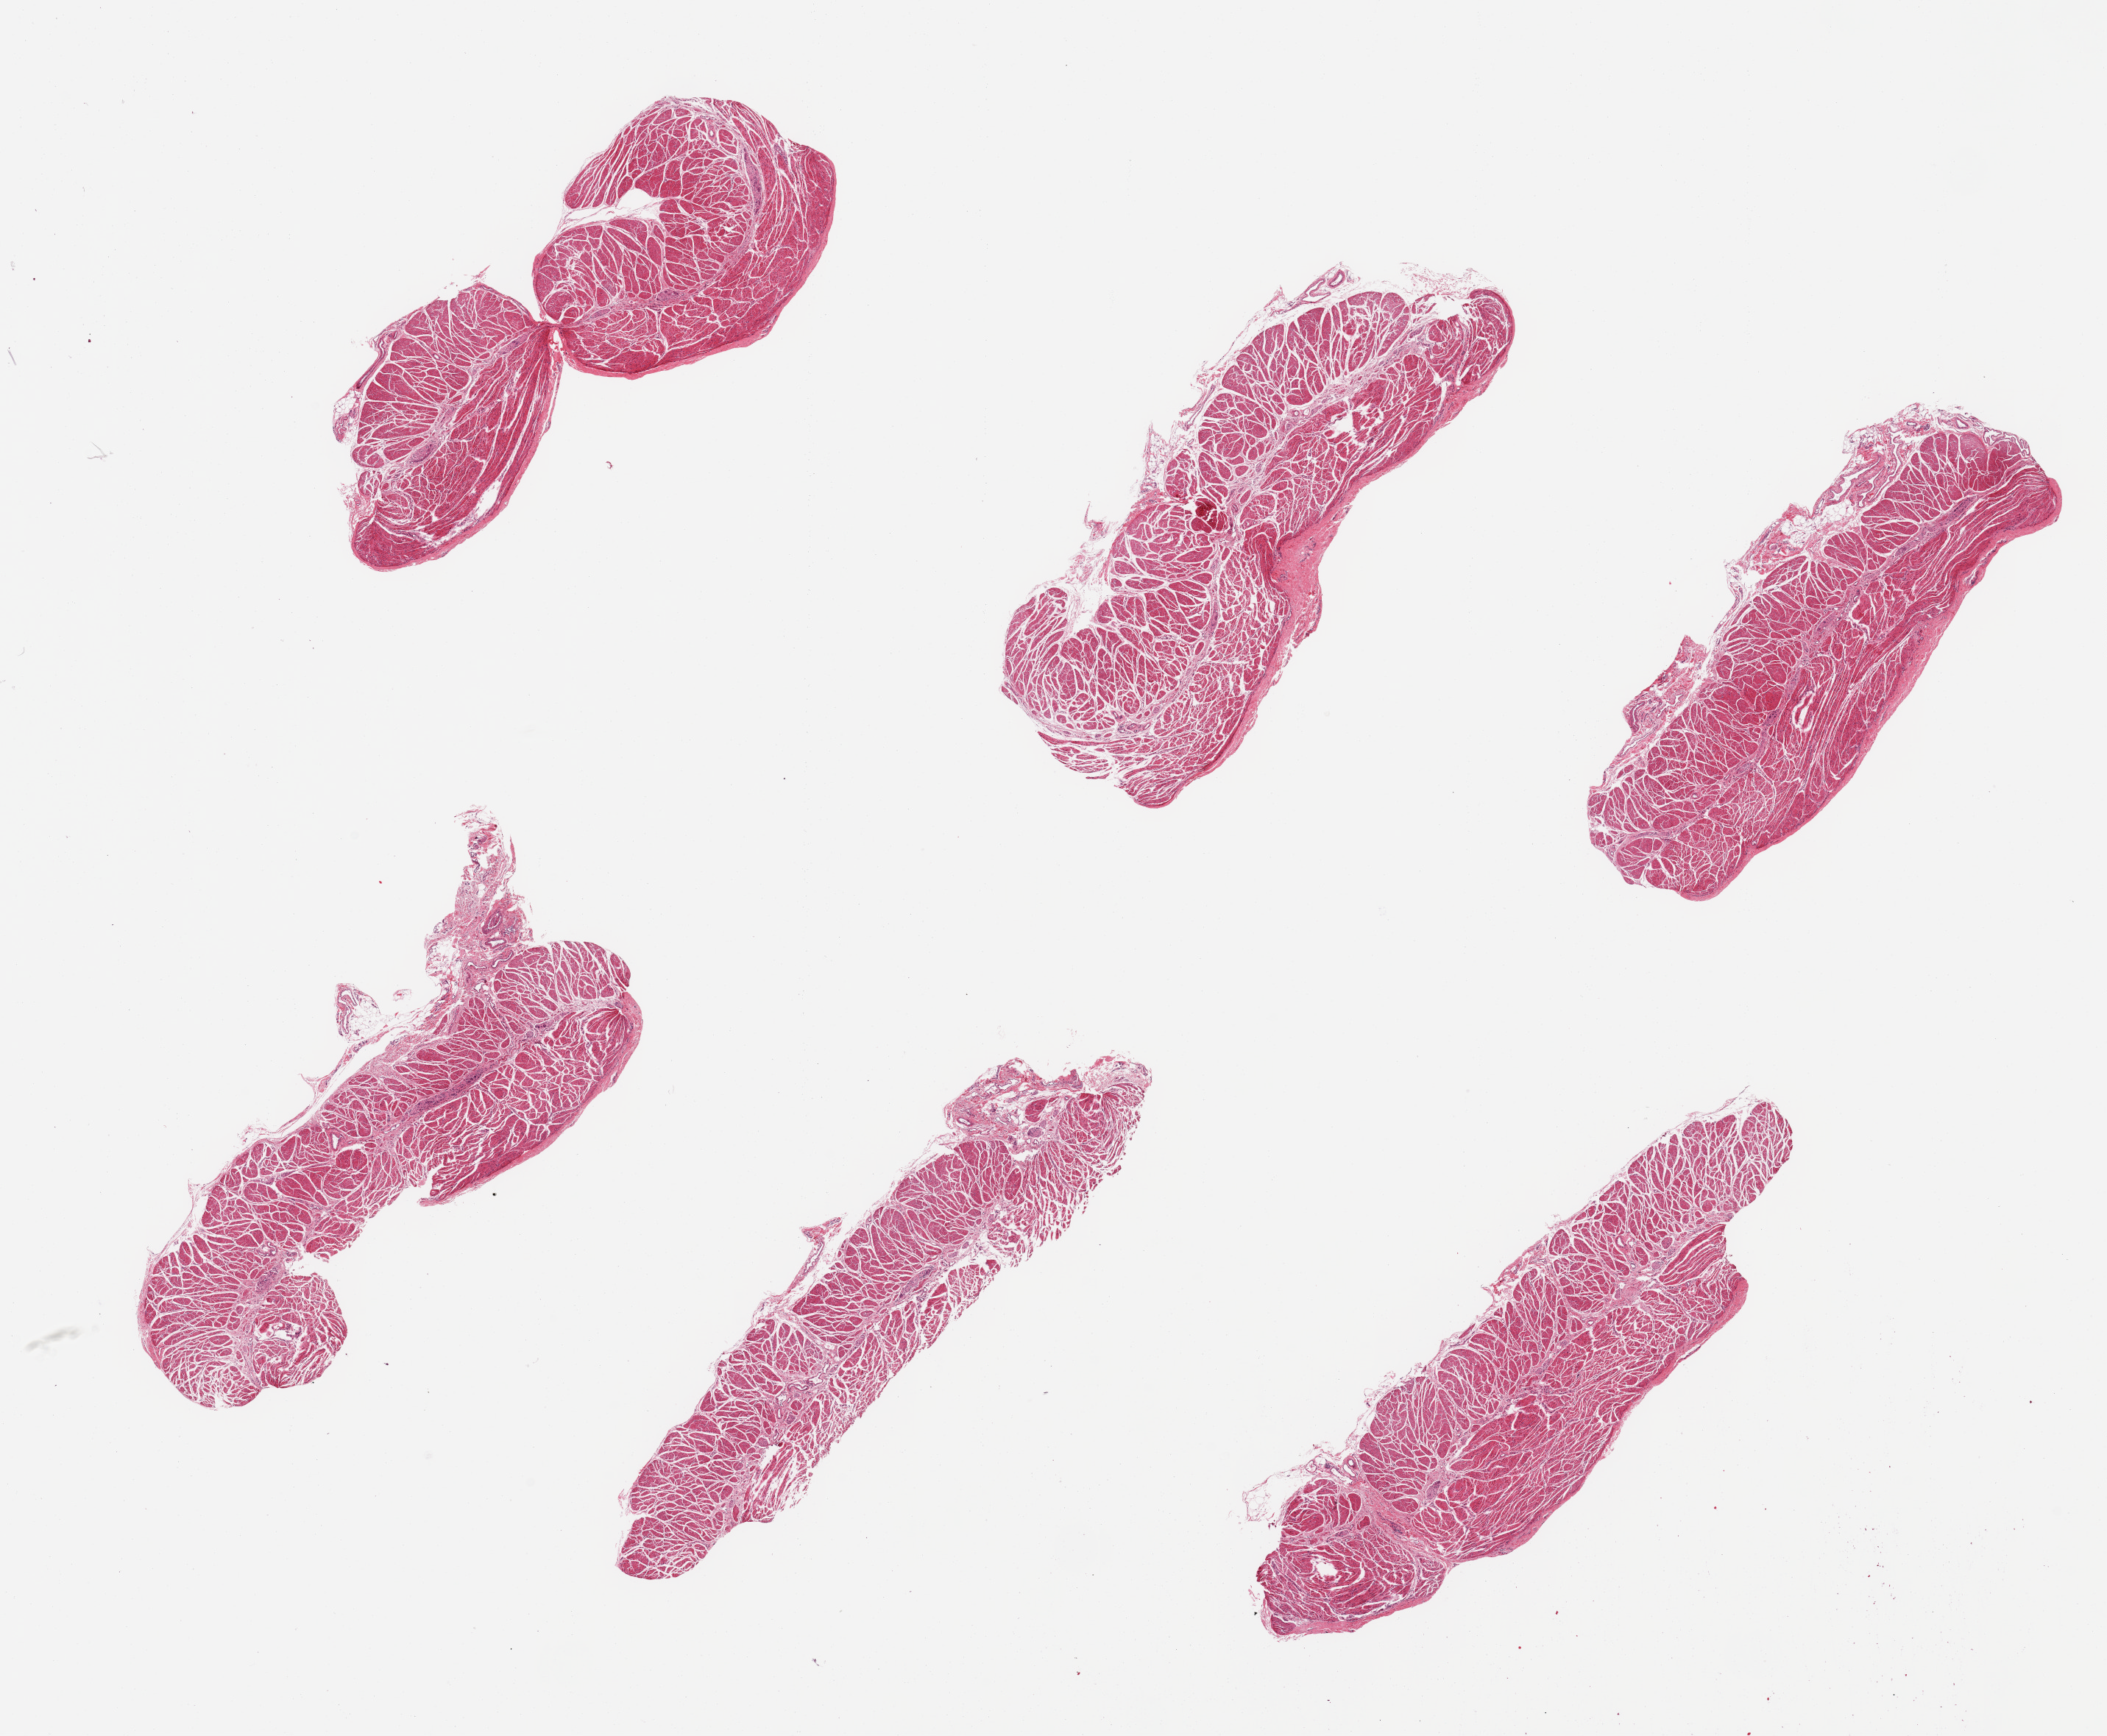
Digitized H&E-stained section, shown as a low-resolution overview of the whole scanned area (about 22.6 x 18.7 mm), PAXgene-fixed, paraffin-embedded tissue, section of gastroesophageal junction (target tissue), donor tissue sample. Female donor.
Reviewer comment on this tissue sample: 6 pieces; well dissected.